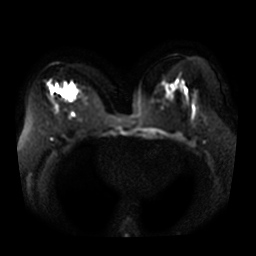
Breast MRI, one axial slice; slice 19 of 36 in the series (ordered by position); diffusion-weighted series; image 2 of 4 stored at this slice position (different b-values; order by instance number); 3 T; 5 mm slice thickness; 256 × 256 image matrix. Female patient.
Outlined on this slice (manually delineated by an expert):
- tumour on diffusion-weighted imaging: bounding box (x1, y1, x2, y2) in pixels: (64, 89, 77, 101)